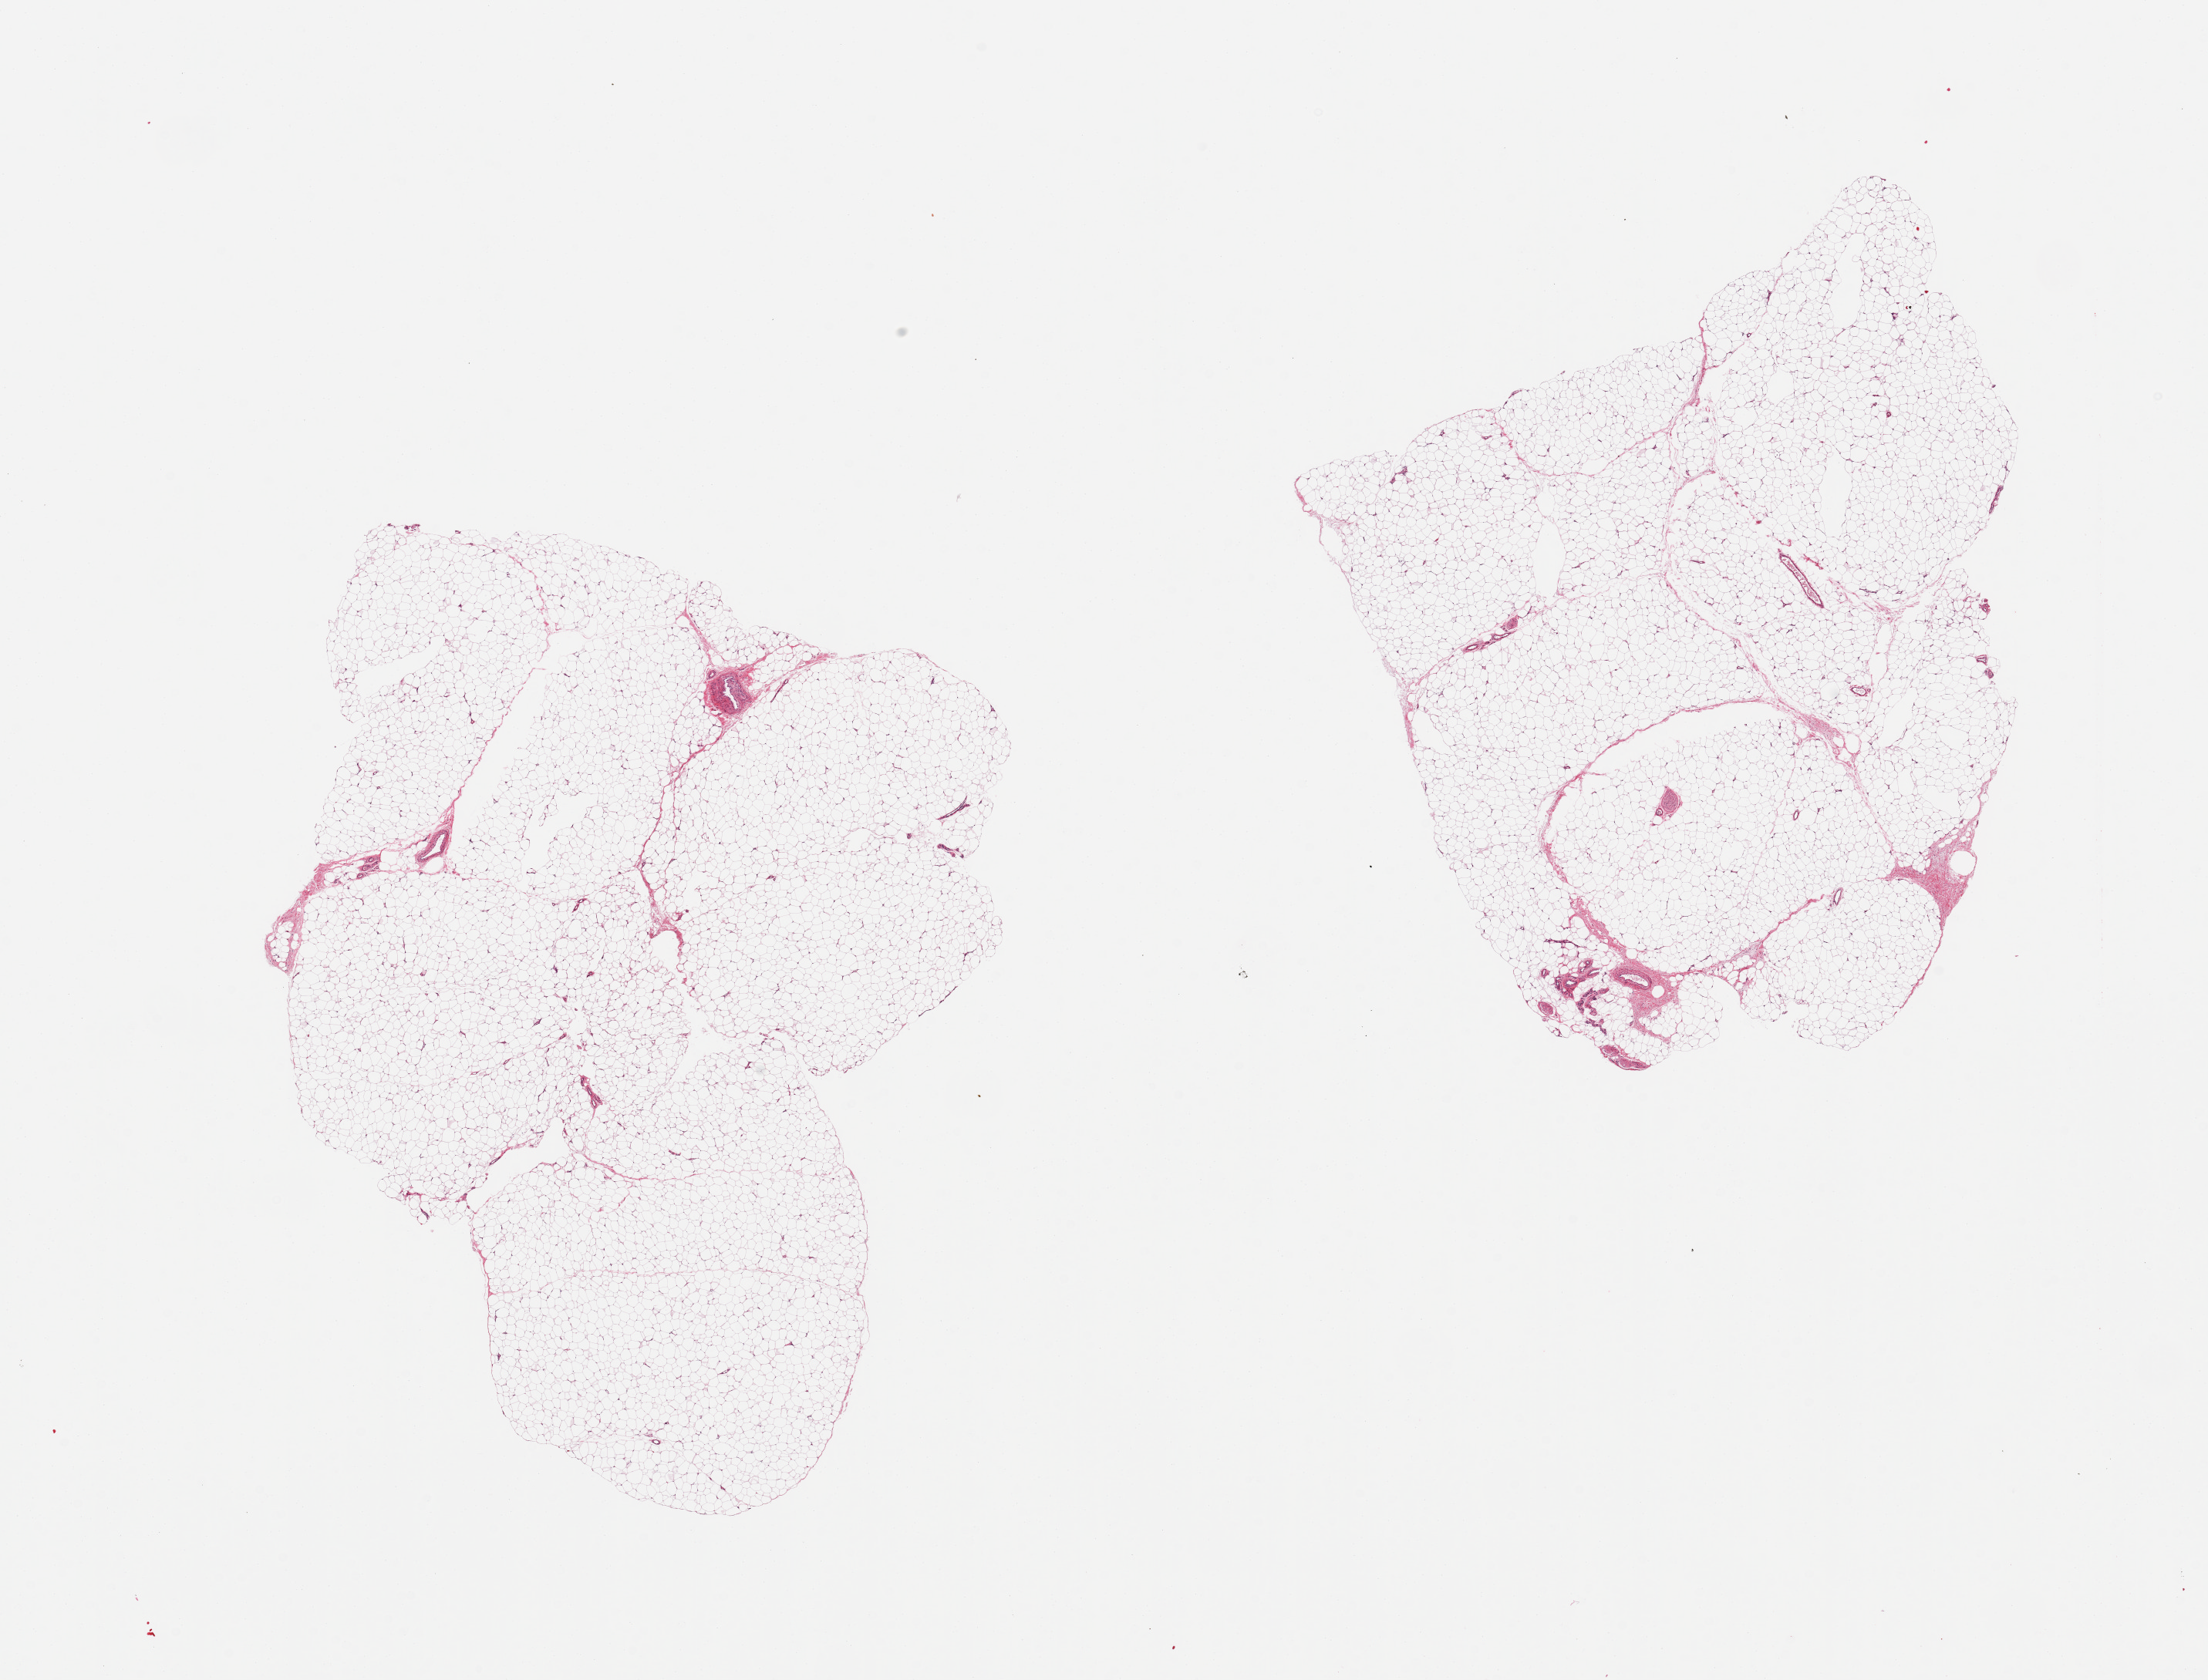
H&E whole-slide image — a low-resolution overview of the entire scanned area, about 22.6 x 17.2 mm (slide scanned at 20x), PAXgene-fixed, paraffin-embedded tissue, section of adipose tissue (target tissue), donor tissue sample. Female donor.
Review note (as recorded): 2 pieces, vascular/fascia elements are <5% of tissue.